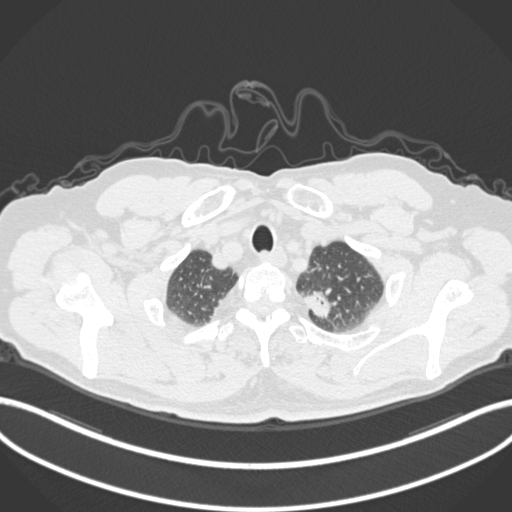
Chest CT, one axial slice; reconstruction kernel B30f; 120 kVp; lung window (W 1500 / L -600 HU); 1 mm slice thickness; 512 × 512 image matrix, field of view 400 × 400 mm. Patient: male, 64 years. Case-level facts recorded for this patient, not image findings: clinical TNM (as recorded): T1c N0 M0.
Annotated regions visible in this slice (rectangle marked by the reading radiologist):
- lung tumour (recorded histology: adenocarcinoma): bounding box [x1, y1, x2, y2] px = [301, 286, 337, 321]